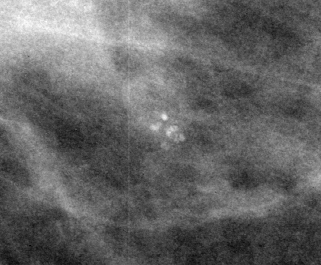
Cropped region of a digitized screen-film mammogram centred on a radiologist-marked abnormality; left breast; MLO view.
- Calcifications, morphology pleomorphic, distribution clustered; BI-RADS assessment category 4; subtlety rating 3 on a 1 (subtle) to 5 (obvious) scale; pathology (as recorded): benign.